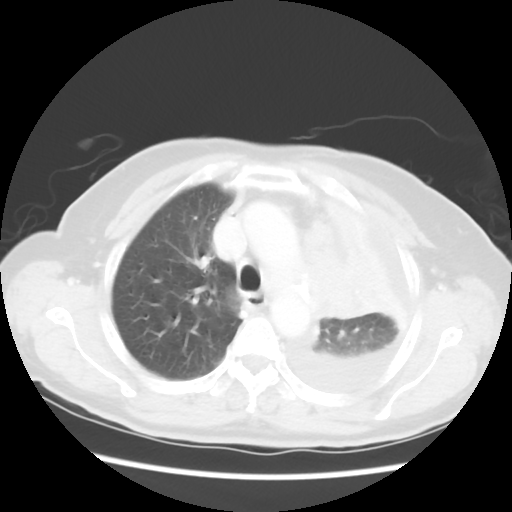
Chest CT, one axial slice. Slice 39 of 52 in the series (ordered by position). Reconstruction kernel STANDARD. 120 kVp. Lung window (W 1500 / L -600 HU). 5 mm slice thickness. 512 × 512 image matrix. Female patient, age 72 years. From the clinical record (not read from this slice): clinical TNM (as recorded): T4 N3 M1b; histopathological grade: G3.
Annotated regions visible in this slice (rectangle marked by the reading radiologist):
- lung tumour (recorded histology: large cell carcinoma): box from (x=309, y=248) to (x=368, y=327) px